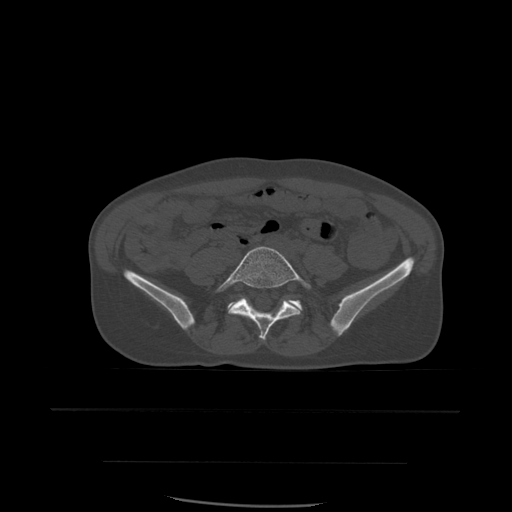
CT including the spine, one axial slice; slice 145 of 574 in the series (ordered by position); bone window (W 1800 / L 400 HU); 512 × 512 image matrix. Patient age 48 years. Case-level facts recorded for this patient, not image findings: primary cancer: lung.
Annotated regions visible in this slice (semi-automatic segmentation, software-assisted and operator-edited):
- L5 vertebra: box from (x=215, y=246) to (x=312, y=341) px